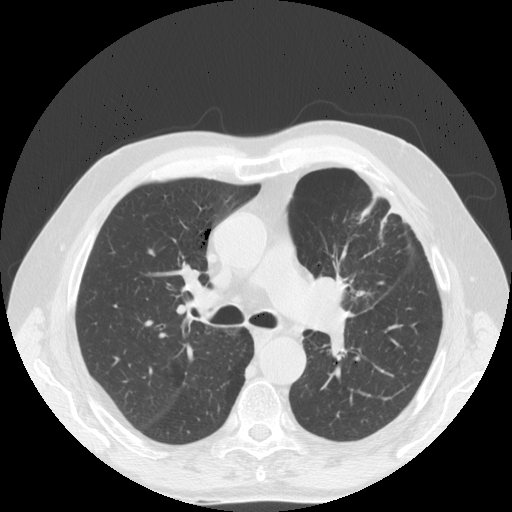
Low-dose screening chest CT, axial slice, first (baseline) screen, lung window (W 1500 / L -600 HU). Male, age 70 years at enrolment. Former smoker at enrolment.
Expert reader's lesion annotation, box from (x=289, y=253) to (x=376, y=344) px. The exam's reader record, not a measurement of the box and not confirmed to be the same lesion: non-calcified nodule or mass ≥4 mm, left upper lobe, 46 × 31 mm, spiculated (stellate) margins, soft tissue attenuation. Official screen result: positive, change unspecified: nodule(s) >= 4 mm or enlarging nodule(s), mass(es), or other non-specific abnormalities suspicious for lung cancer. Later outcome: lung cancer diagnosed 78 days after this screen — squamous cell carcinoma, NOS, left upper lobe, poorly differentiated (G3), stage IIIB (AJCC 6th edition), 46 mm at pathology.